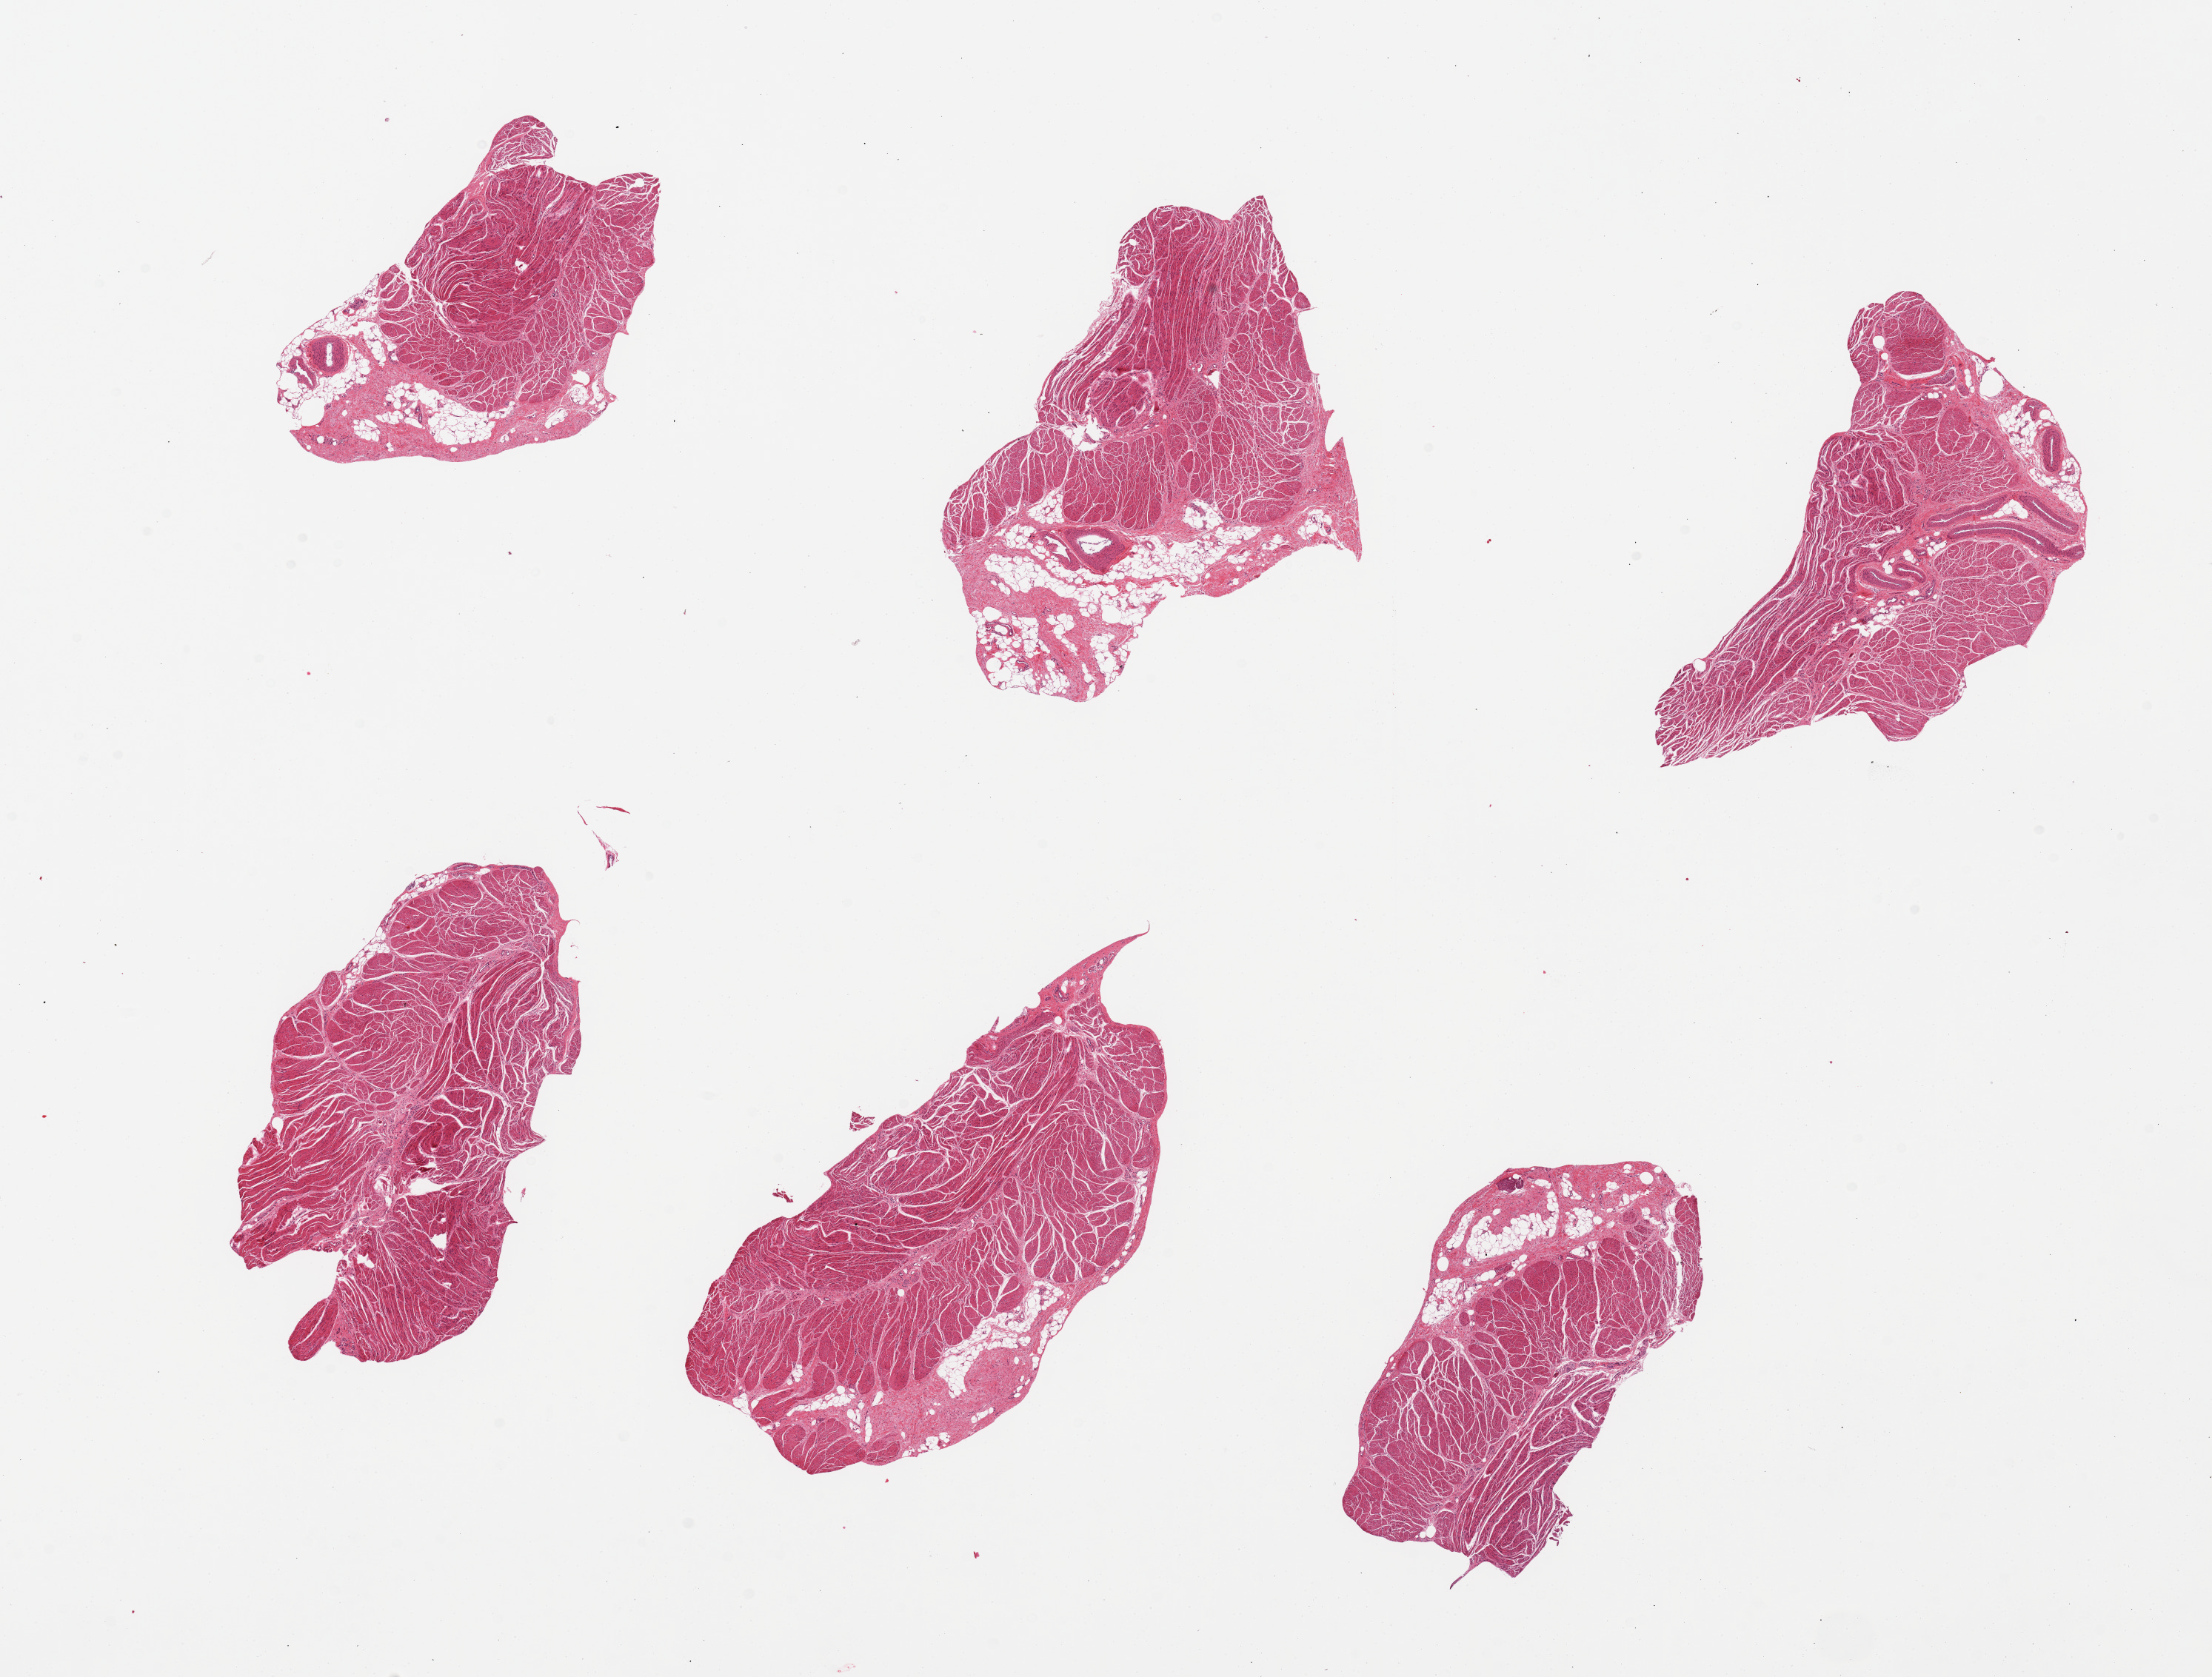
Digitized haematoxylin and eosin-stained section, shown as a low-resolution overview of the whole scanned area (about 23.6 x 17.9 mm, slide scanned at 20x); PAXgene-fixed, paraffin-embedded tissue; sampled site (target tissue): gastroesophageal junction; tissue donor sample. Donor sex: female.
- pathologist's review note for this sample: 6 pieces, small focus of squamous mucosa, may not be present in block